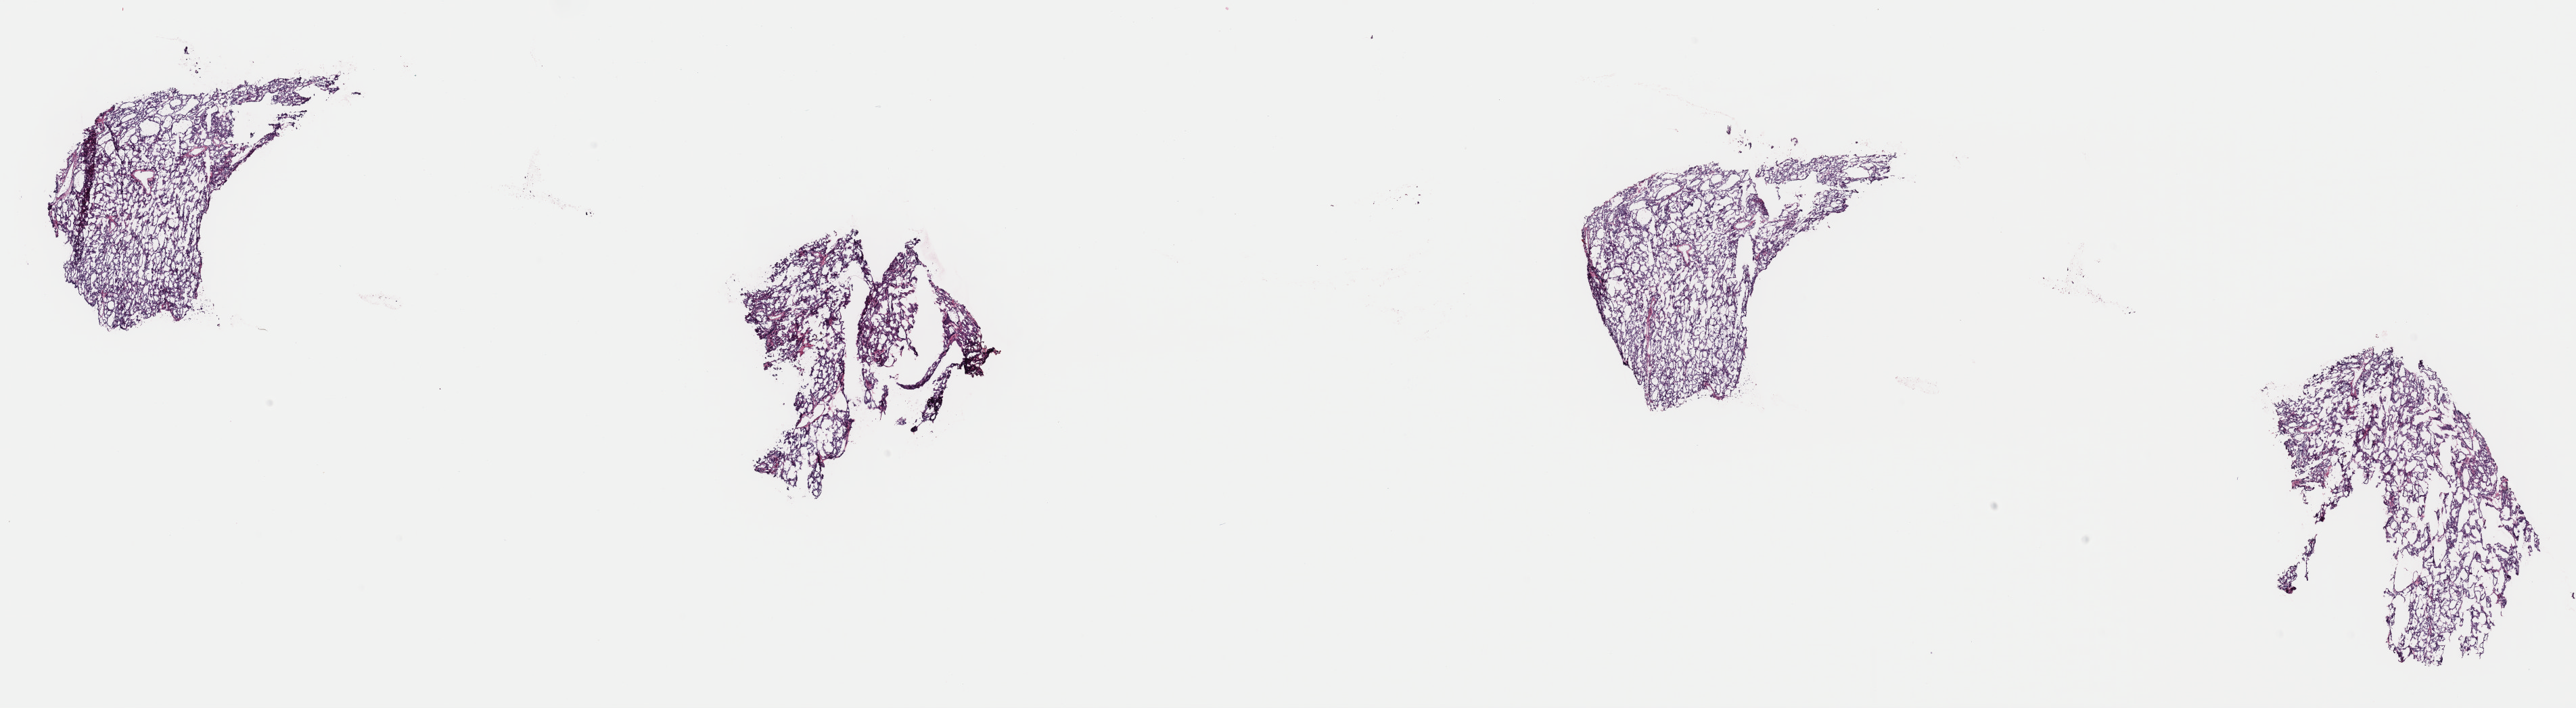
Digitized H&E tissue section (whole slide) — whole scanned area (about 30.1 x 8.3 mm) shown as a low-resolution overview. Frozen section from the top of the tissue portion. Thyroid, primary tumour sample. Male, age 78 years at initial diagnosis. Composition of this section per pathologist review: tumour cells 90%, tumour nuclei 100%, normal cells 0%, stromal cells 10%, necrosis 0%. Inflammatory infiltration, as recorded: lymphocyte infiltration 0%, monocyte infiltration 2%, neutrophil infiltration 0%.
• AJCC pathologic stage: III (7th edition)
• pathologic diagnosis: Papillary adenocarcinoma, NOS (thyroid gland)